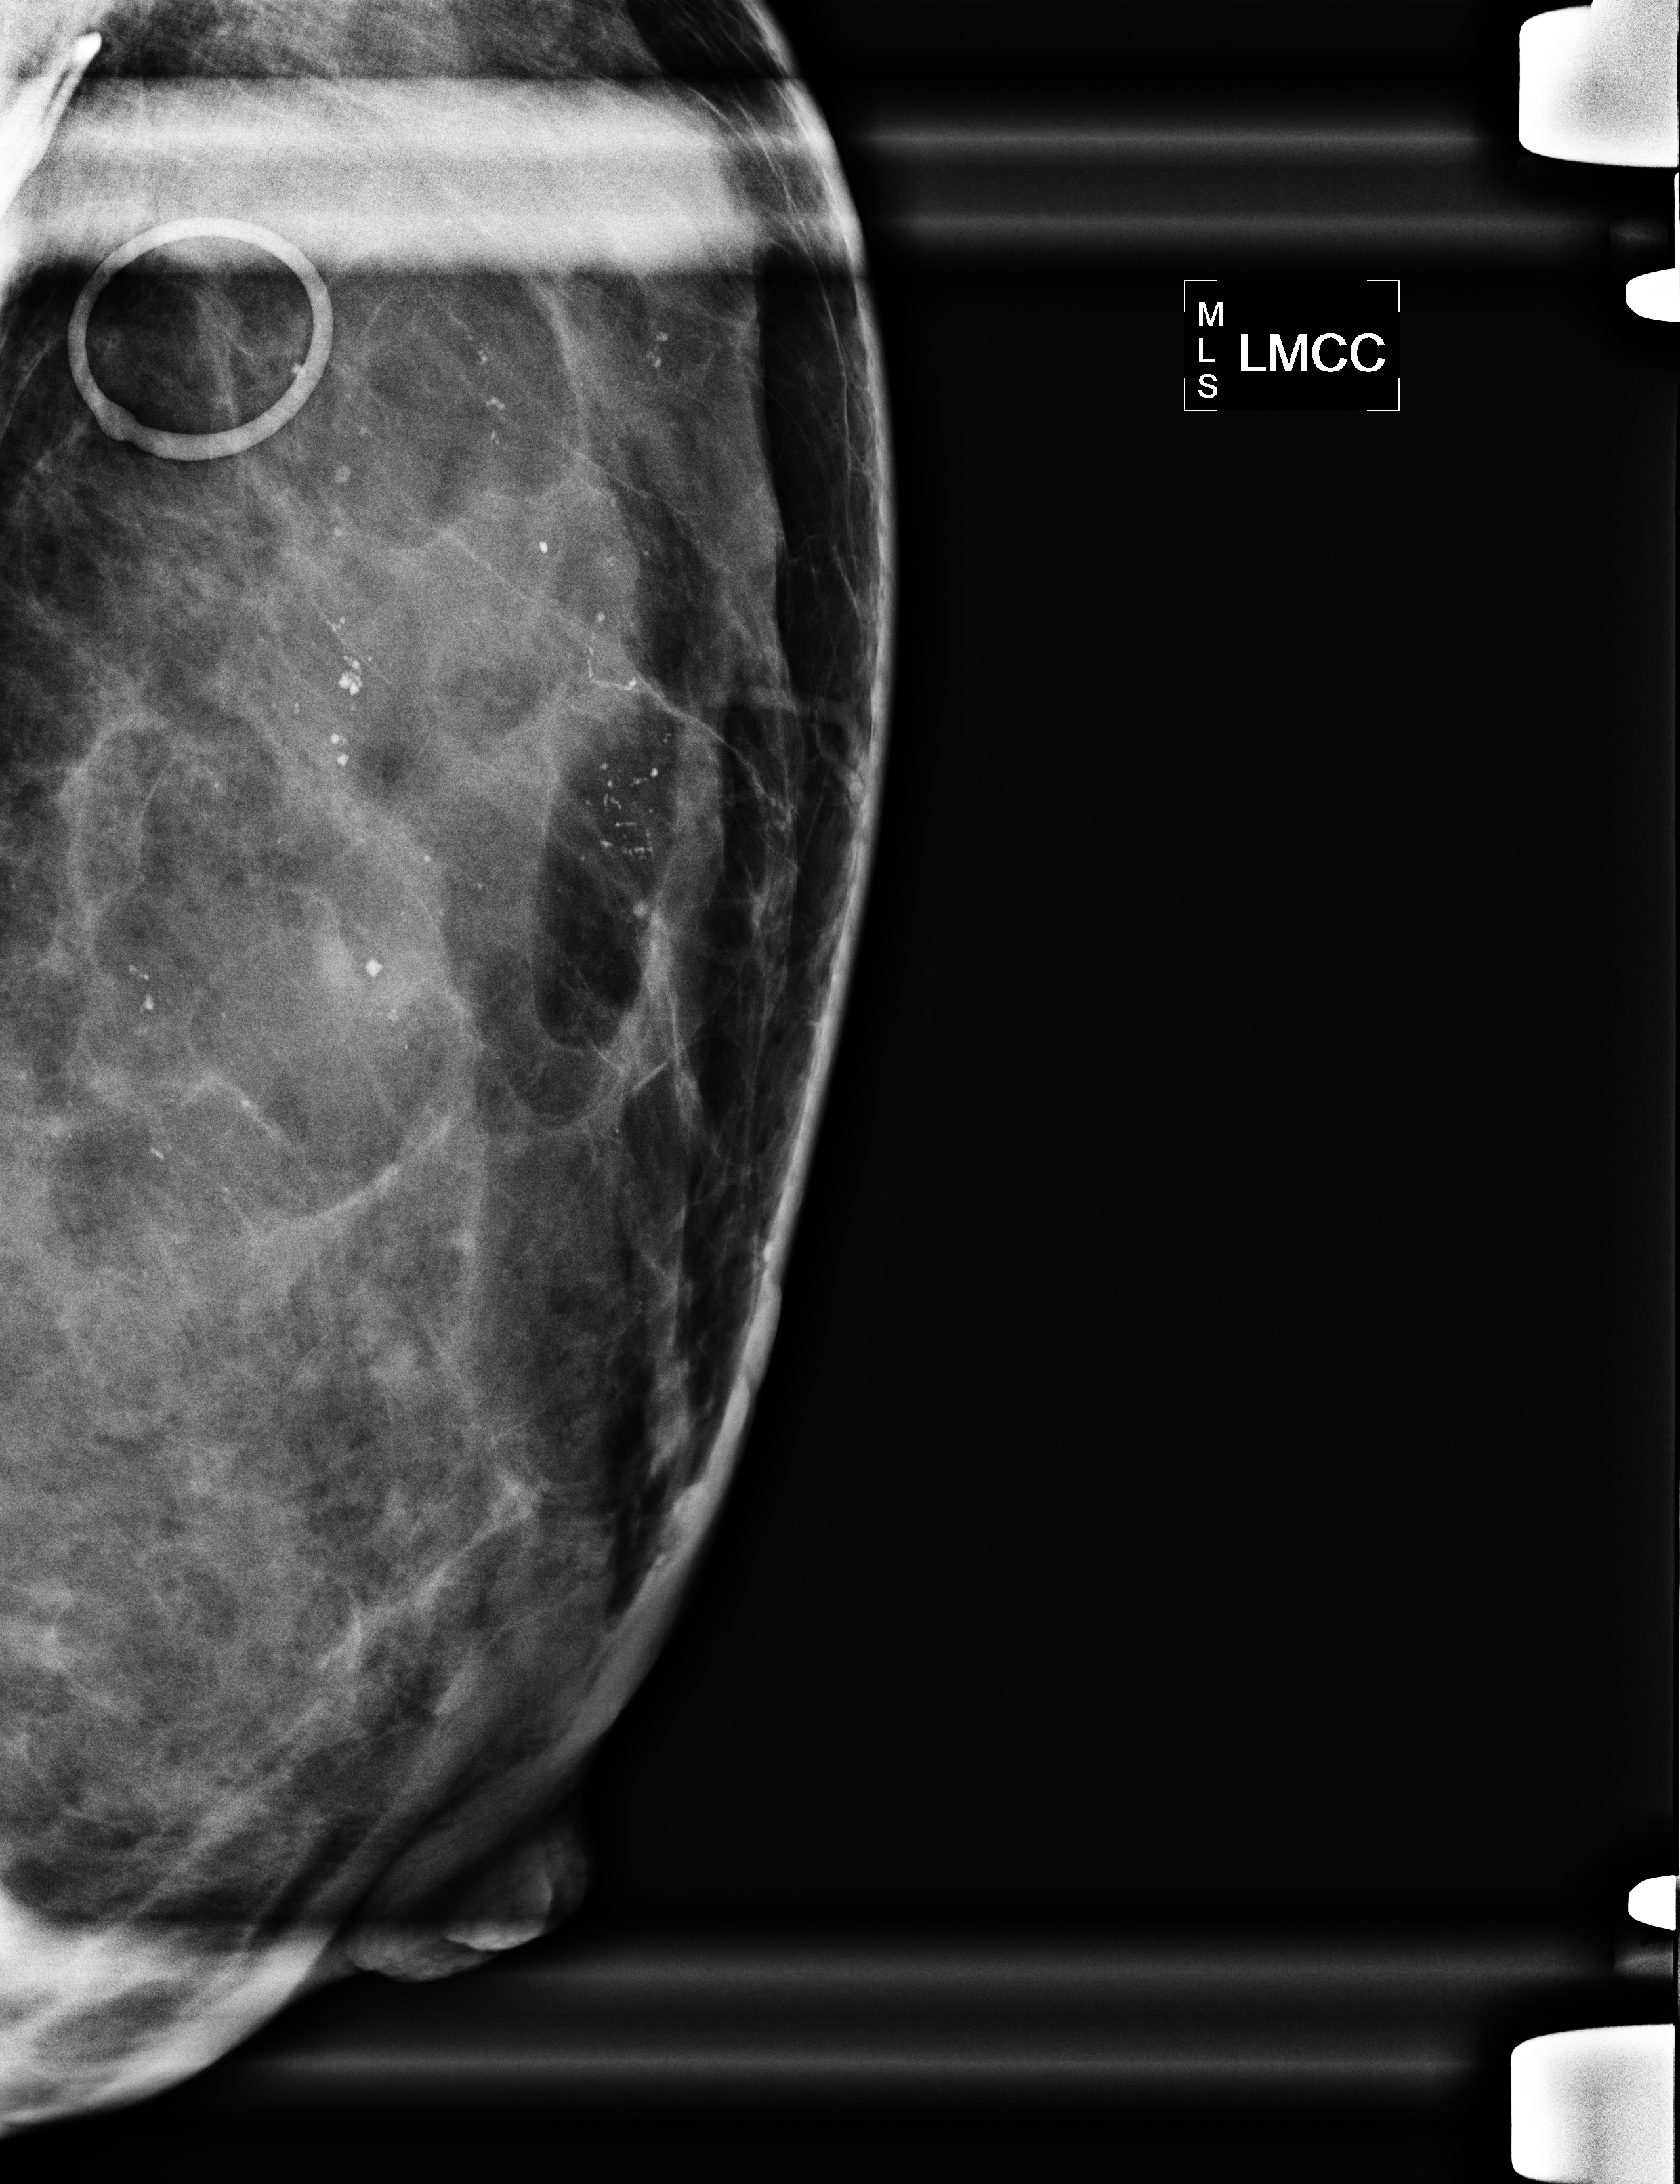
Mammogram, left breast, CC view; patient in her 50s.
Pathology recorded for this patient (not read from this image): pathology diagnosis: specimen: INVASIVE CARCINOMA. Lymph nodes reactive but neg (left breast); receptor status (as recorded): ER neg, PR neg, HER2 neg; Ki-67 (as recorded): pos hi prolif (49% nucs); pathology report notes: The tumor exhibits extensive mucinous features, however high nuclear grade is not a characteristic finding in cases of mucinous carcinoma, and therefore, the tumor is best classified as invasive ductal carcinoma with mucinous features; clinical background (as recorded): history of right mastectomy
for cancer presents for her first 6 month follow up for calcifications
in her left breast and a left breast nodule.